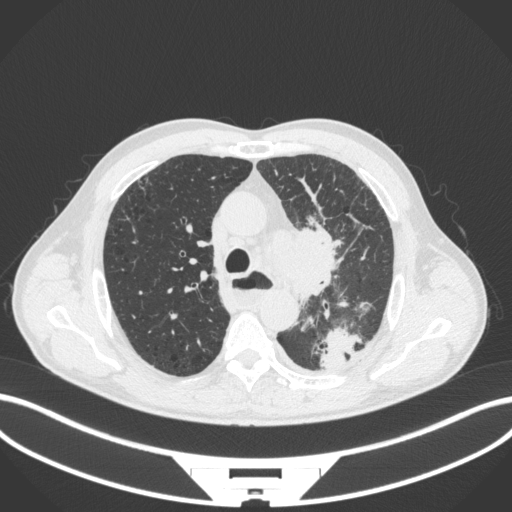
Chest CT, one axial slice; slice 269 of 411 in the series (ordered by position); reconstruction kernel B31f; 120 kVp; lung window (W 1500 / L -600 HU); 1 mm slice thickness; 512 × 512 image matrix, field of view 400 × 400 mm. Male patient, age 57 years. Case-level facts recorded for this patient, not image findings: clinical TNM (as recorded): T2a N1 M0.
Outlined on this slice (rectangle marked by the reading radiologist):
- lung tumour (recorded histology: squamous cell carcinoma): bounding box [x1, y1, x2, y2] px = [262, 216, 348, 303]